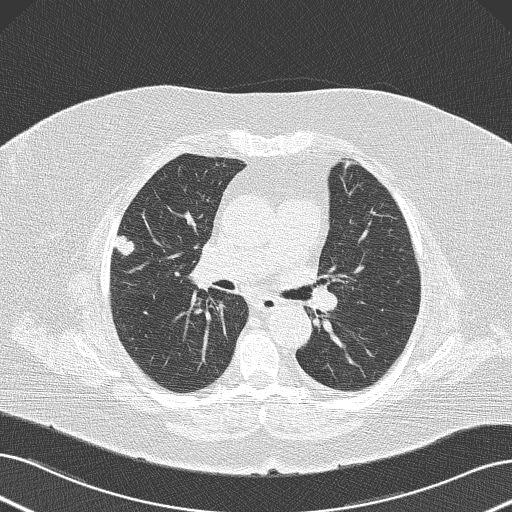
Chest CT (low-dose screening protocol), one axial image, baseline annual screen, lung window (W 1500 / L -600 HU), 120 kVp, 512 × 512 image matrix, field of view 364 × 364 mm. Female, age 73 years at enrolment. Former smoker at enrolment.
Expert reader's lesion annotation, bounding box (x1, y1, x2, y2) in pixels: (103, 221, 148, 262). Screening reader's record for this exam (one nodule recorded; not confirmed to be the boxed lesion): non-calcified nodule or mass ≥4 mm, right upper lobe, 15 × 11 mm, poorly defined margins, soft tissue attenuation. Official screen result: positive, change unspecified: nodule(s) >= 4 mm or enlarging nodule(s), mass(es), or other non-specific abnormalities suspicious for lung cancer. Participant outcome: lung cancer diagnosed 55 days after this screen — neoplasm, malignant, right upper lobe, stage IA (AJCC 6th edition), 15 mm at pathology.